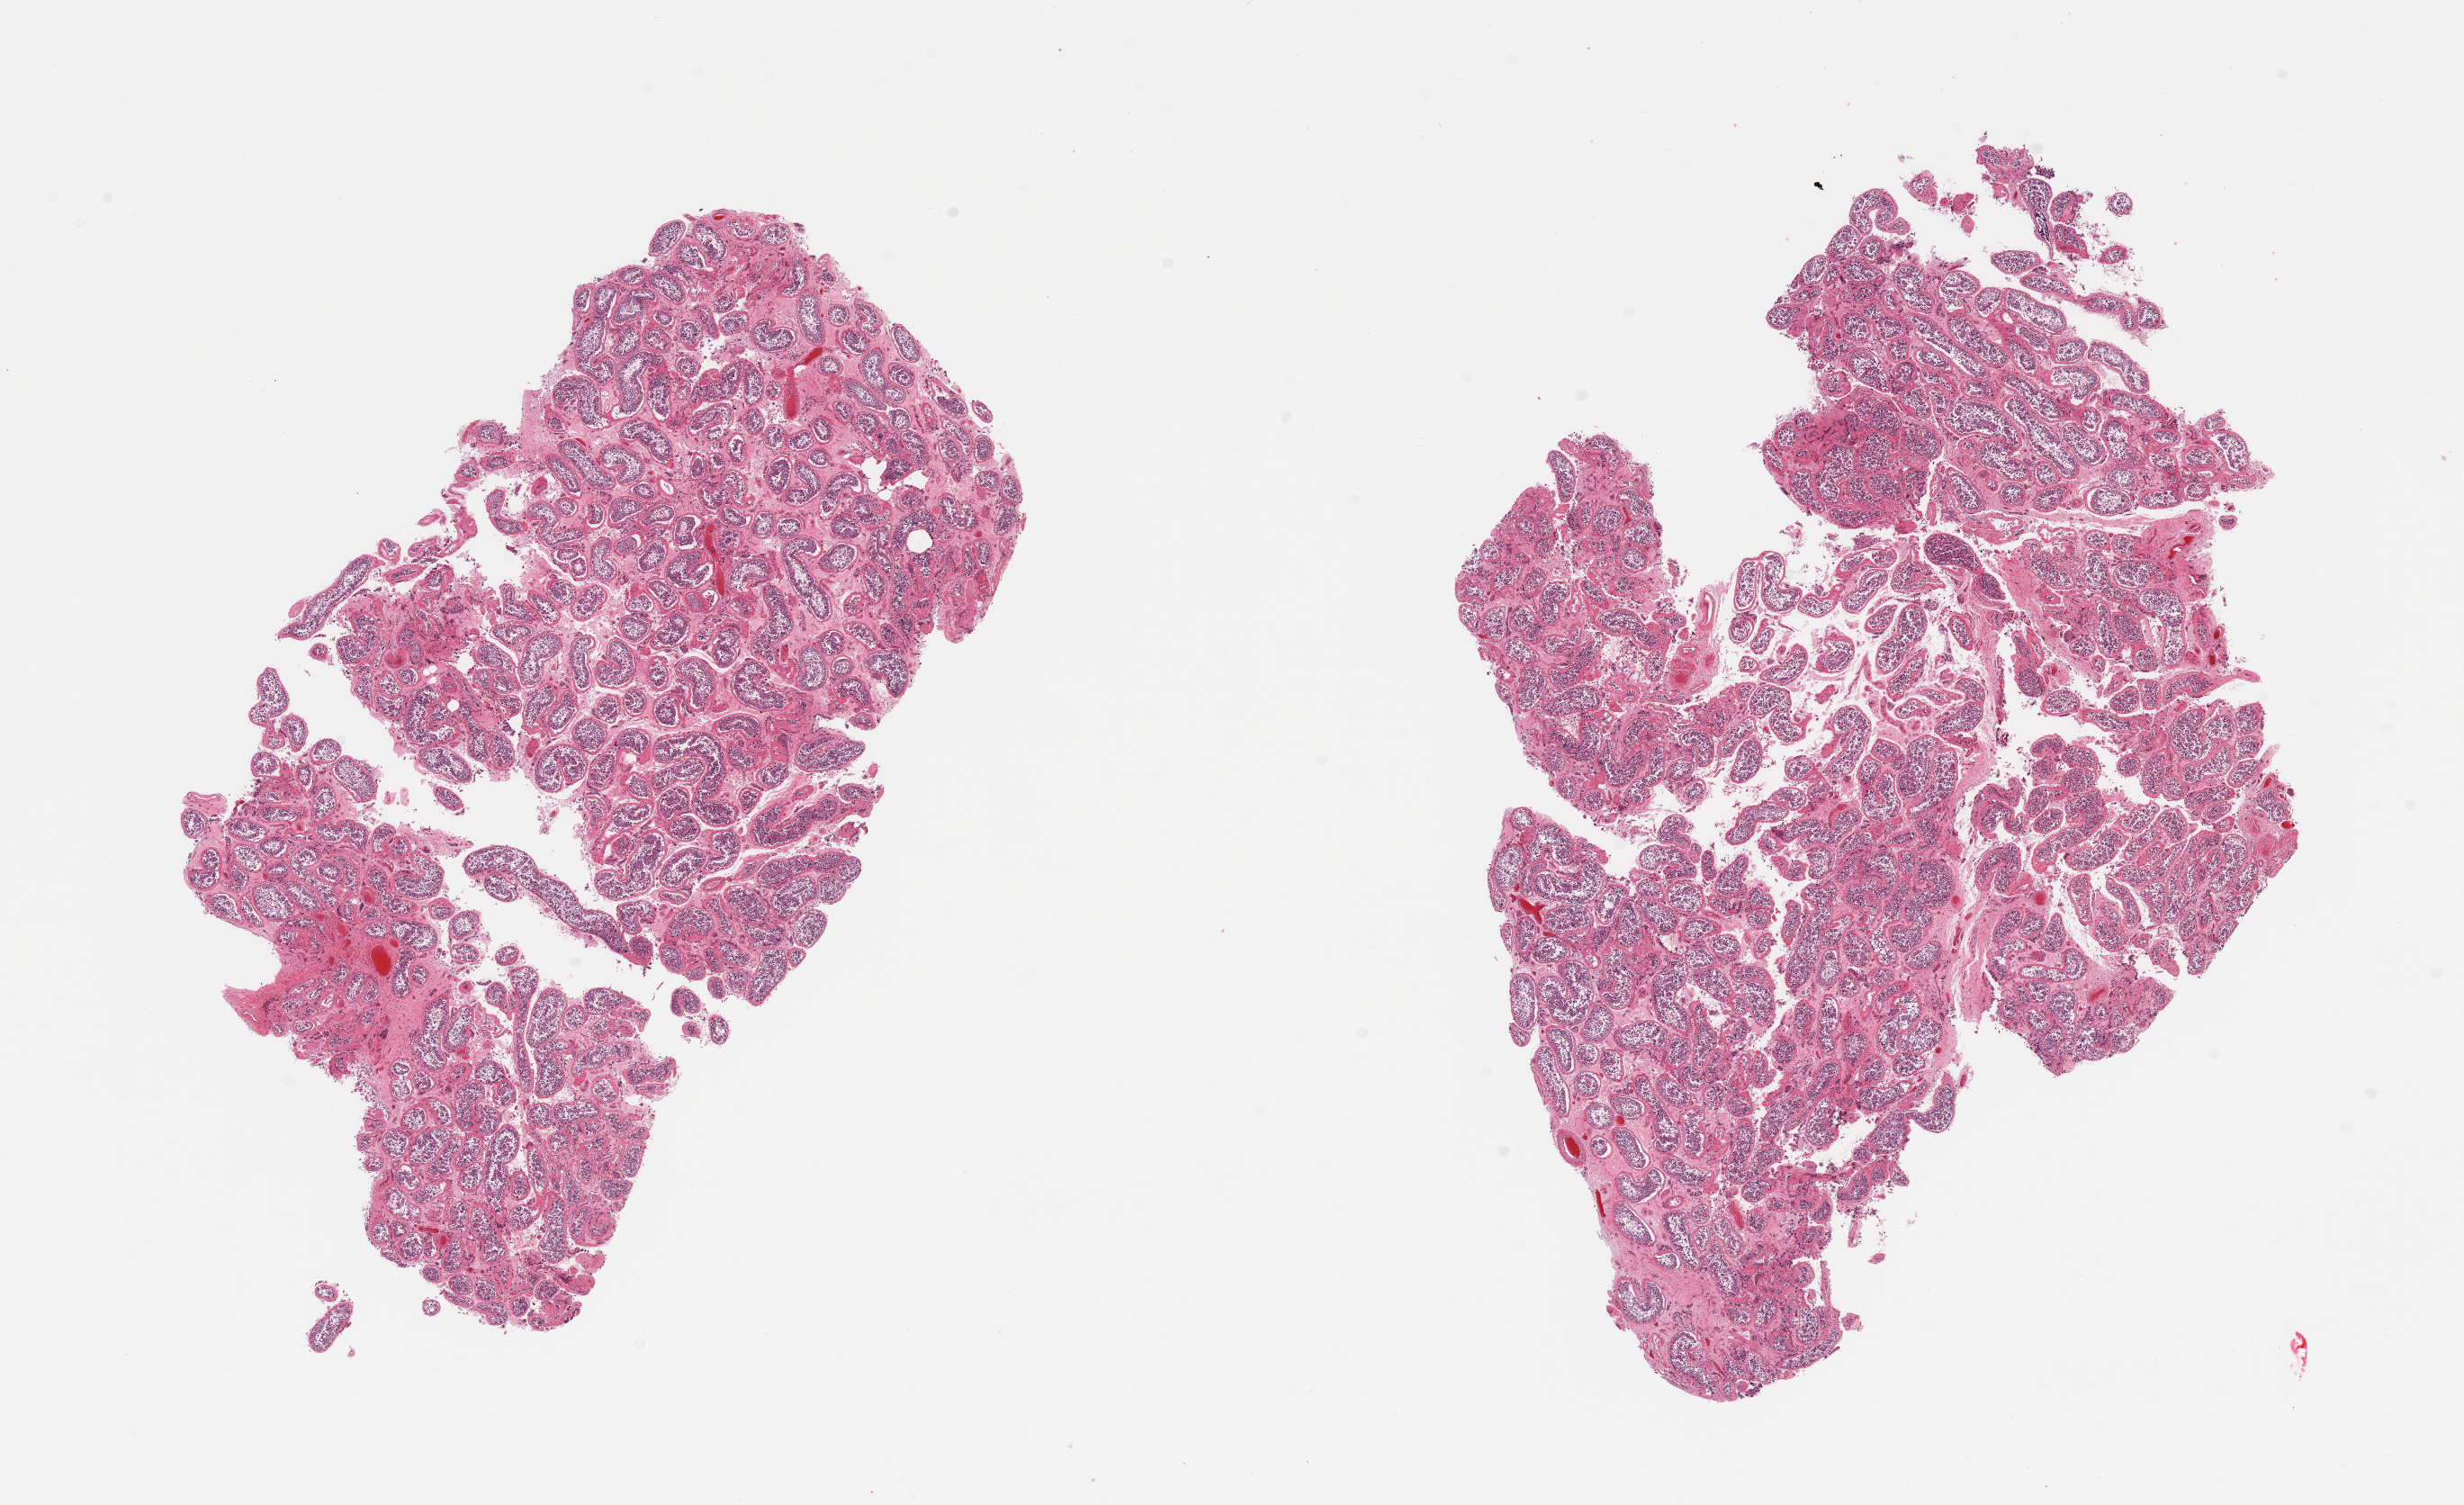
Haematoxylin and eosin whole-slide image — shown as a low-resolution overview of the whole scanned area (about 21.7 x 13.2 mm), PAXgene-fixed paraffin-embedded (PFPE) section, section of testis (target tissue), donor tissue sample. Donor sex: male.
• review note (as recorded): 2 pieces; spermatogenesis is present/reduced